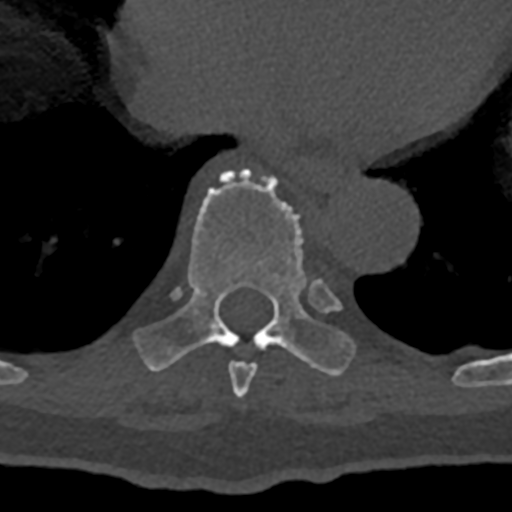
CT including the spine, one axial slice; position 667 of 797 along the scan axis; 120 kVp; bone window (W 1800 / L 400 HU); 0.5 mm slice thickness; 512 × 512 image matrix, field of view 160 × 160 mm. Patient: male, 74 years. From the clinical record (not read from this slice): primary cancer: renal.
Outlined on this slice (semi-automatic segmentation, software-assisted and operator-edited):
- T8 vertebra: bounding box (x1, y1, x2, y2) in pixels: (228, 361, 257, 398)
- T9 vertebra: (133, 169, 356, 376)